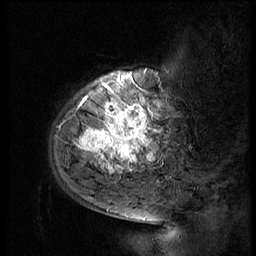
Breast MRI (dynamic contrast-enhanced), one sagittal slice; position 13 of 56 along the scan axis; 3 images stored at this slice position (order not interpretable as contrast timing); 1.5 T; TE 4.2 ms, TR 9 ms; 256 × 256 image matrix. Female patient, age 51 years. From the clinical record (not read from this slice): setting: breast cancer imaged before/during neoadjuvant chemotherapy; receptor status: triple-negative.
Structures marked on this image (semi-automatically segmented with operator editing):
- analysis volume of interest (the breast-tissue region the enhancement analysis was run in; not a lesion): bounding box <52,66,183,179> (left, top, right, bottom; pixels)
- tumour enhancement mask (voxels above the 140 % enhancement threshold inside the analysis volume of interest): <77,78,157,173>